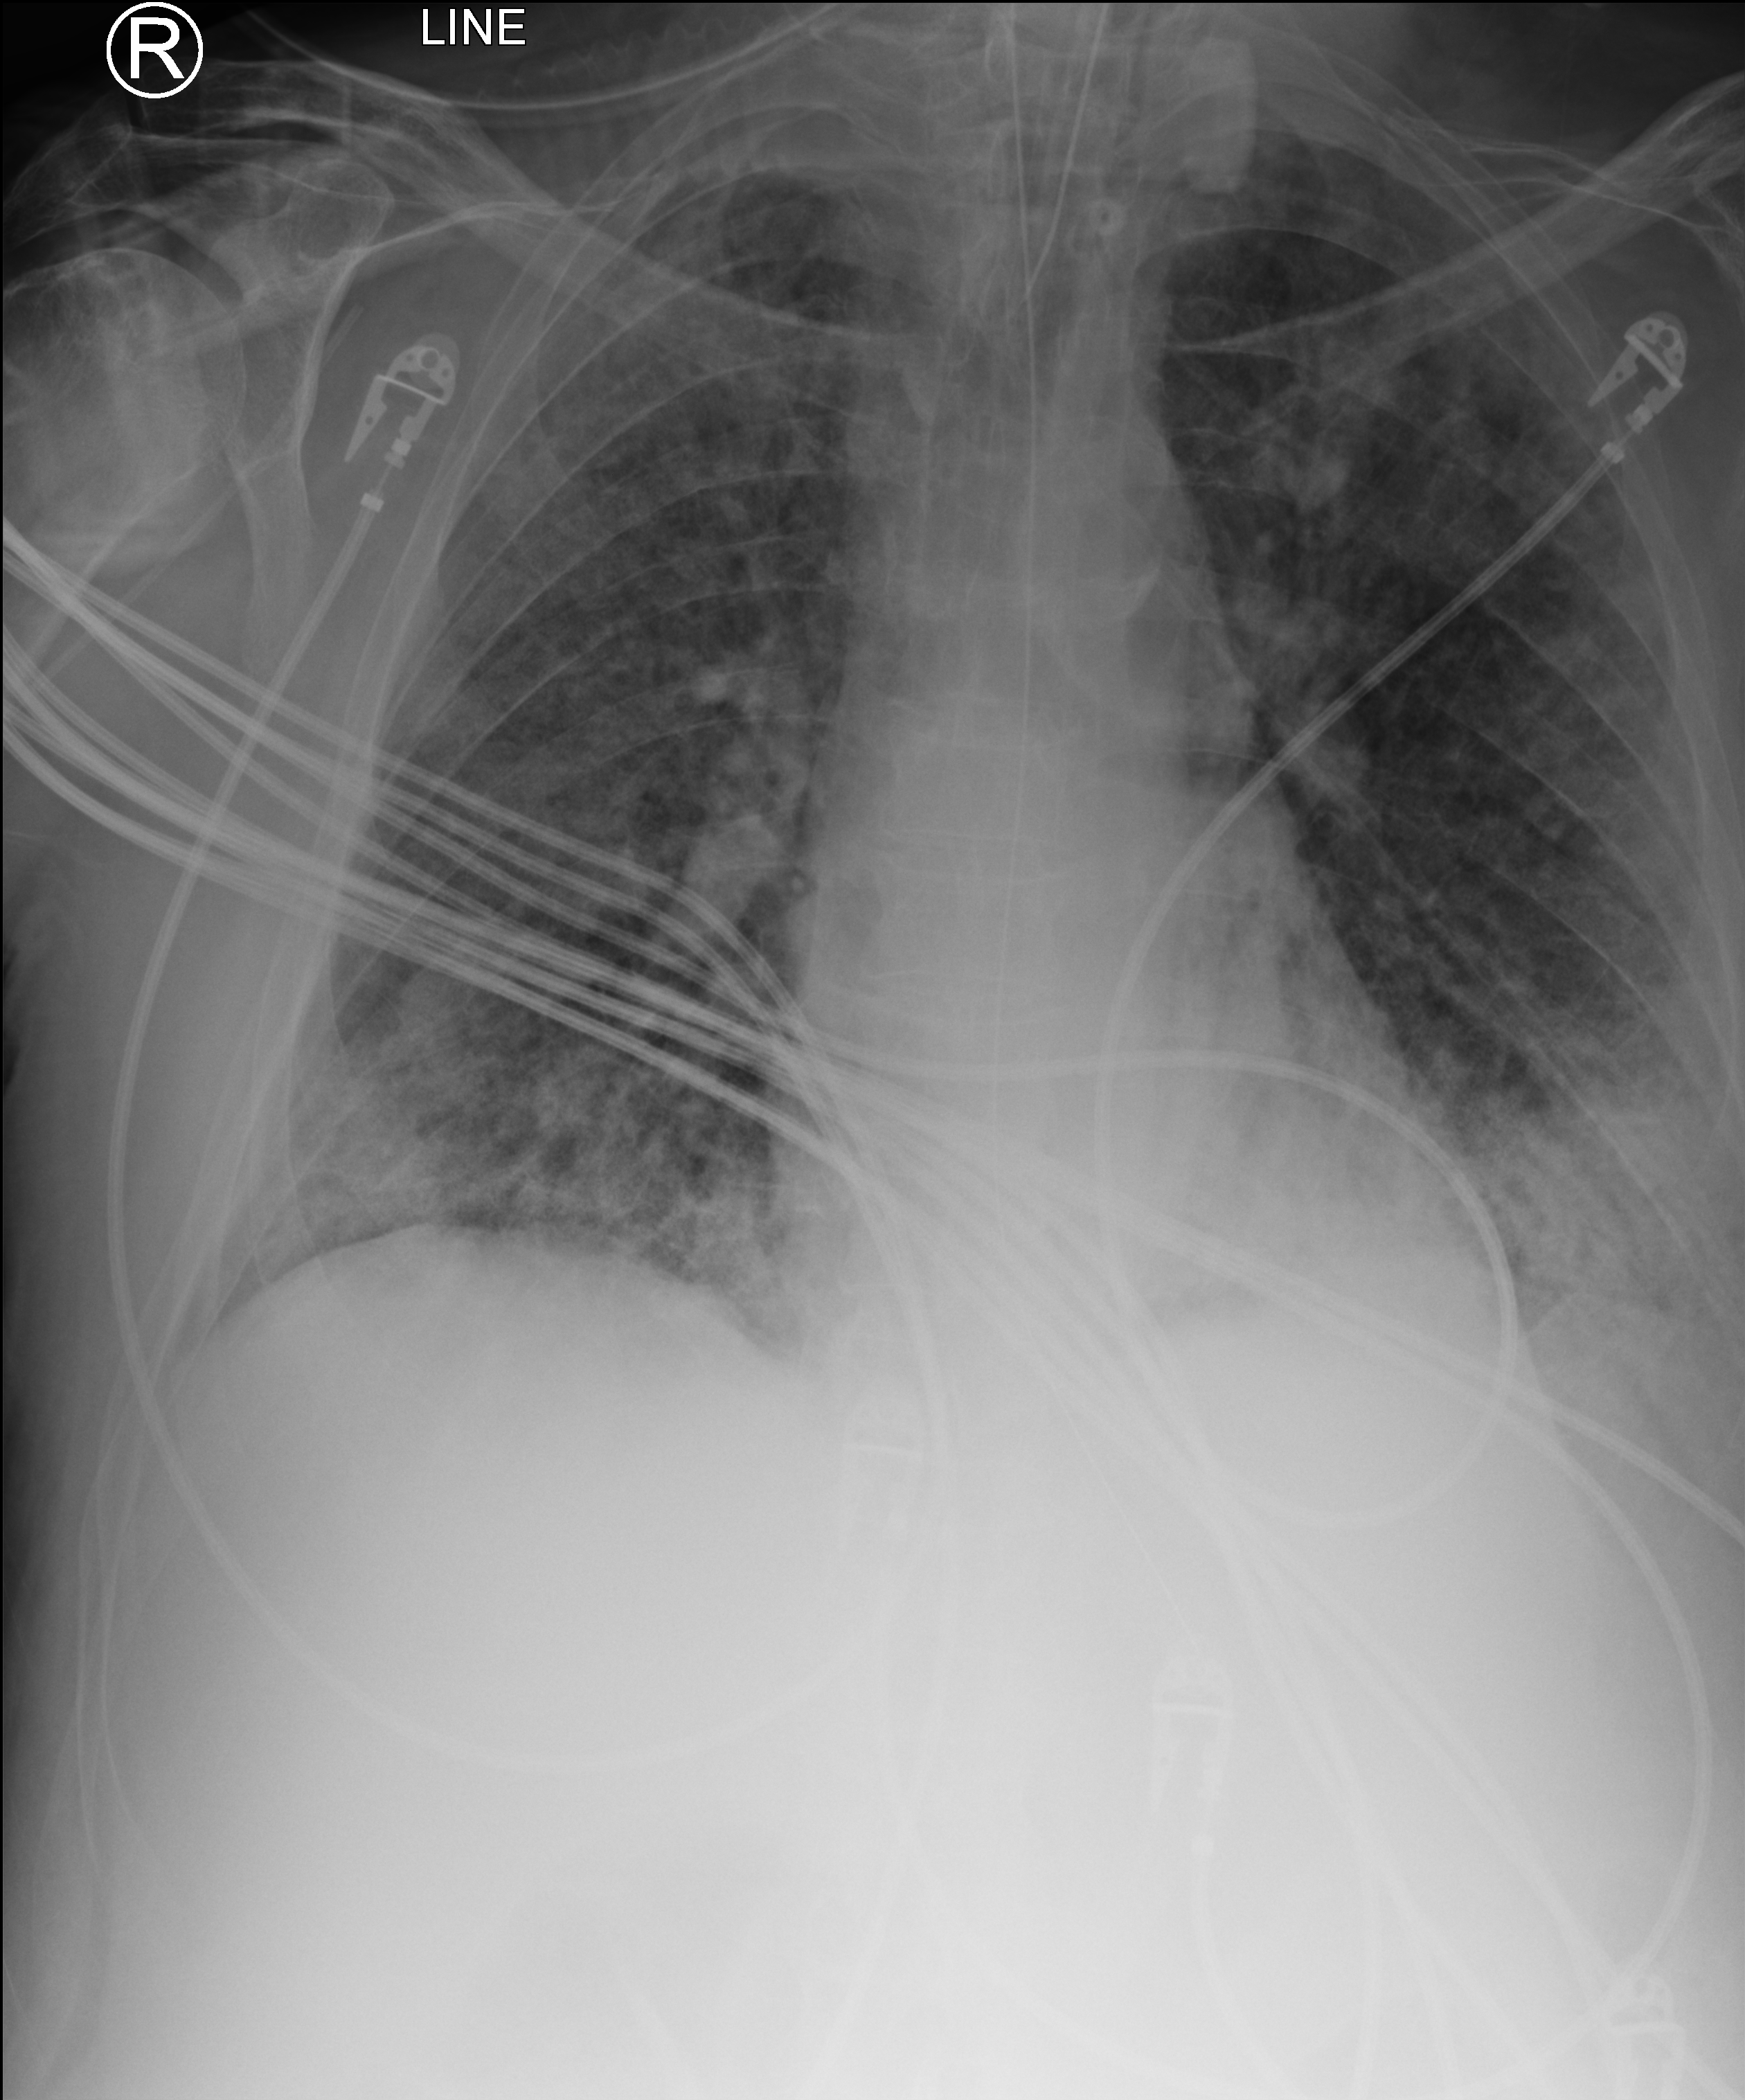
Chest X-ray (portable); anteroposterior (AP) projection. Patient hospitalised with COVID-19; male, aged 60–74 years.
From the hospital-stay record, not from the radiograph (when in the stay this image was taken is not recorded): hypertension (admission record): no; diabetes (admission record): no; other chronic lung disease (admission record): no.